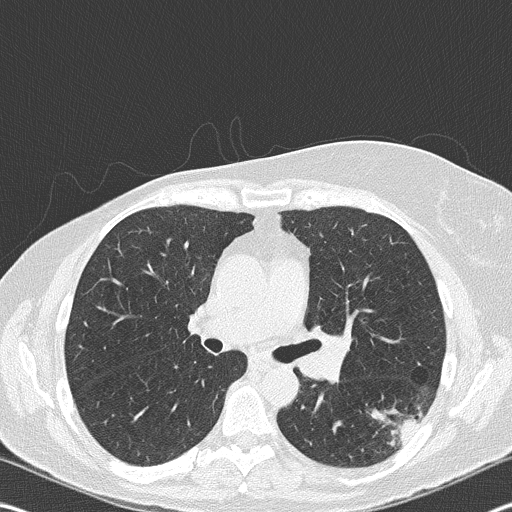
Low-dose screening chest CT, axial slice; second annual screen; lung window (W 1500 / L -600 HU); 2 mm slice thickness; lung (sharp) reconstruction kernel (B50f); slice 107 of 177 in the series; 512 × 512 image matrix, field of view 342 × 342 mm. Female, age 60 years at enrolment. Current smoker at enrolment.
• Lesion marked by an expert reader, bounding box <371,384,439,451> (left, top, right, bottom; pixels).
• Reader record for this screening exam (exam-level; its link to the box is not recorded): non-calcified nodule or mass ≥4 mm, left lower lobe, 18 × 16 mm, spiculated (stellate) margins, soft tissue attenuation, pre-existing on the prior screen: no.
• Official screen result: positive, other.